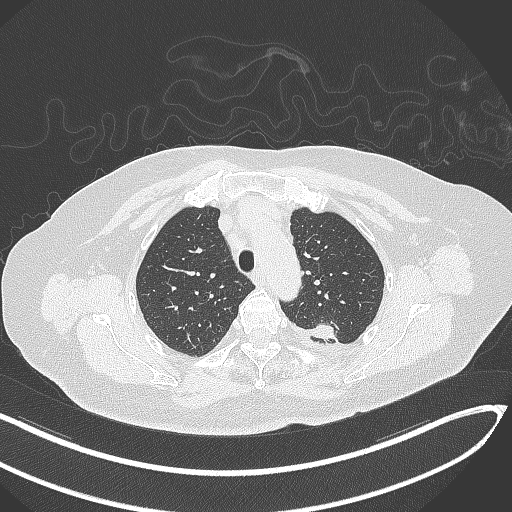
Chest CT, one axial slice; slice 249 of 270 in the series (ordered by position); reconstruction kernel B70f; 120 kVp; lung window (W 1500 / L -600 HU); 1 mm slice thickness; 512 × 512 image matrix, field of view 400 × 400 mm. Patient: female, 76 years. From the clinical record (not read from this slice): clinical TNM (as recorded): T1c N0 M0.
Structures marked on this image (bounding box drawn by a radiologist):
- lung tumour (recorded histology: adenocarcinoma): bounding box <306,321,347,345> (left, top, right, bottom; pixels)